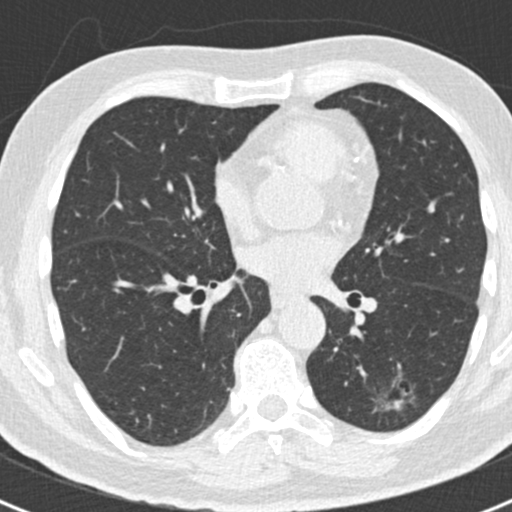
Axial slice from a low-dose chest CT screening exam. First (baseline) screen. Lung window (W 1500 / L -600 HU). 2 mm slice thickness. Standard (soft-tissue) reconstruction kernel (B30f). Slice 90 of 188 in the series. 512 × 512 image matrix. Male participant, aged 66 years at enrolment.
Lesion marked by an expert reader, box from (x=348, y=343) to (x=422, y=422) px. Reader record for this screening exam (exam-level; its link to the box is not recorded): non-calcified nodule or mass ≥4 mm, left lower lobe, 43 × 27 mm, smooth margins. Official screen result: positive, change unspecified: nodule(s) >= 4 mm or enlarging nodule(s), mass(es), or other non-specific abnormalities suspicious for lung cancer. Lung cancer was diagnosed 801 days after this screen: adenocarcinoma, NOS, left lower lobe, poorly differentiated (G3), stage IB (AJCC 6th edition), 38 mm at pathology.